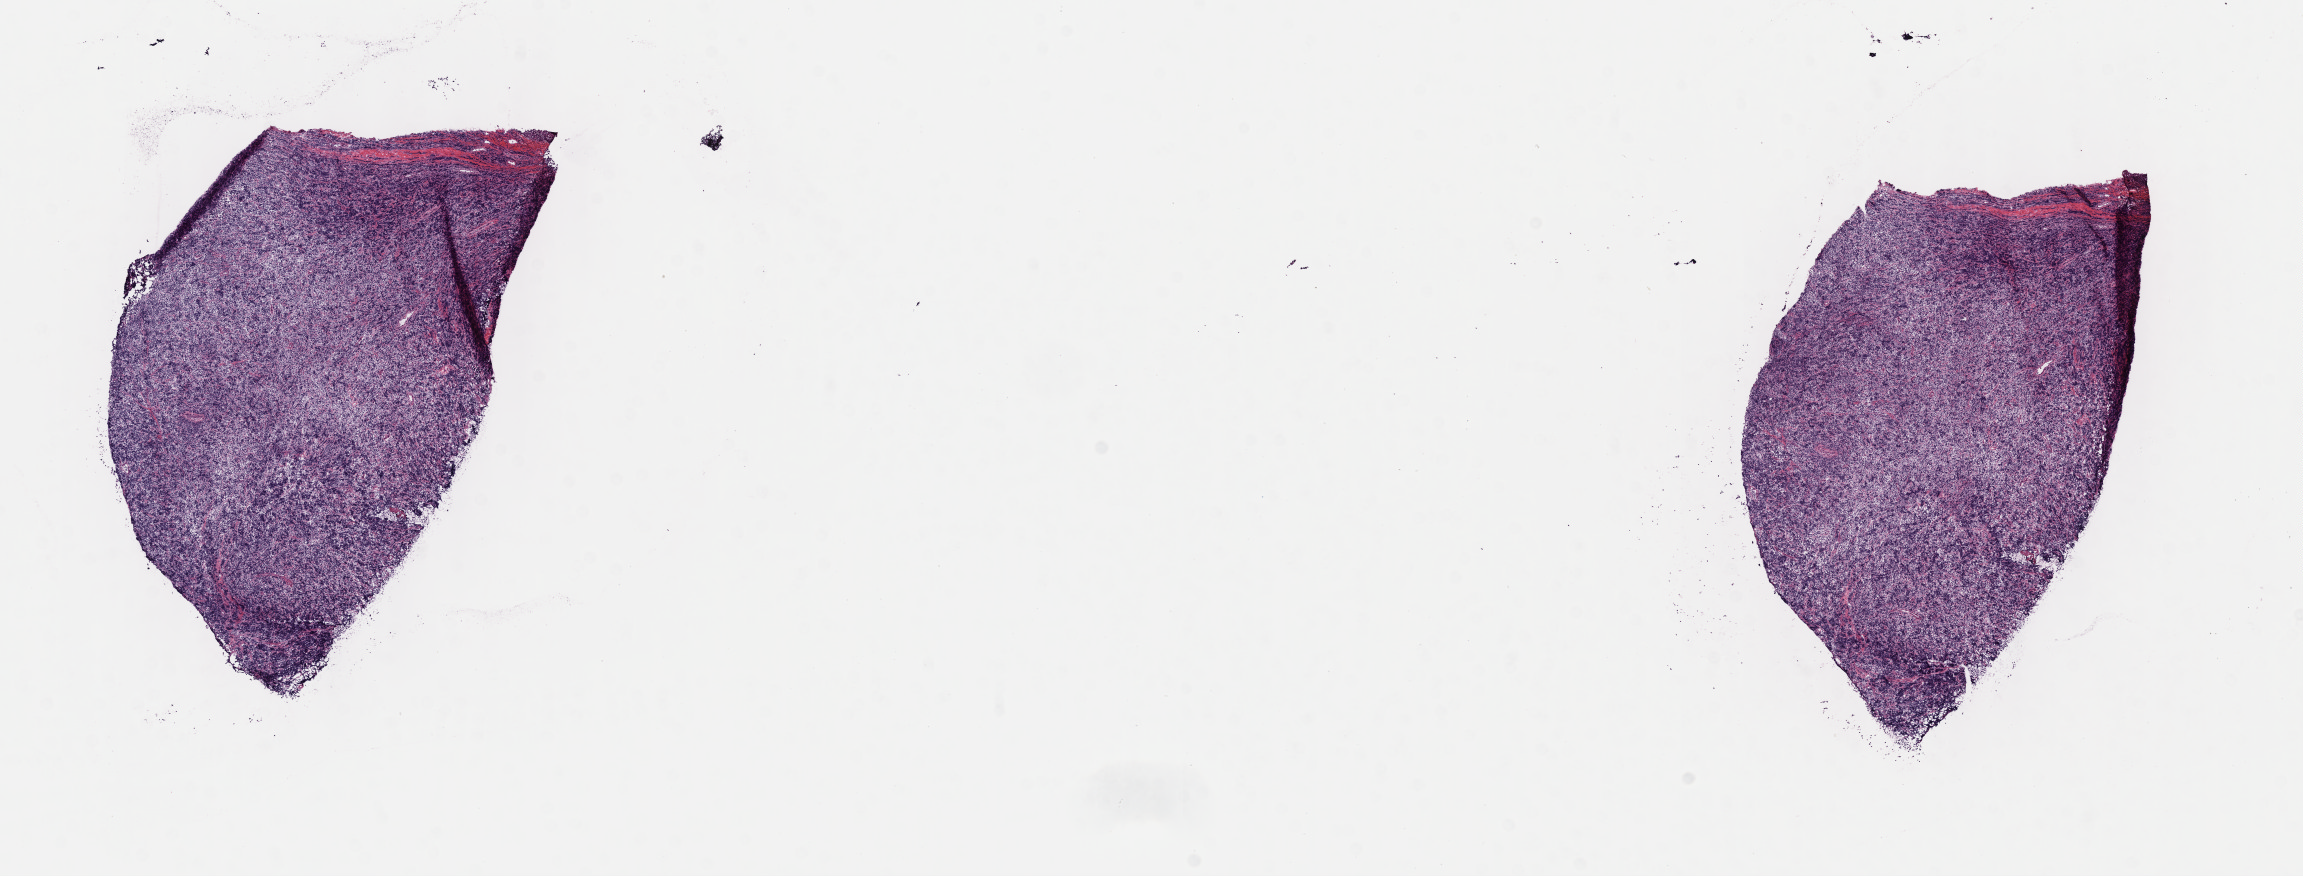
Hematoxylin and eosin (H&E) whole-slide image — a low-resolution overview of the entire scanned area, about 18.6 x 7.1 mm; frozen section; specimen: primary tumor; anatomic site: cranium. Patient: male, age at initial diagnosis 6 years. Composition of this section per pathologist review: tumor cells 90%, tumor nuclei 90%, stromal cells 7%, necrosis 3%, normal cells 0%. Inflammatory infiltration, as recorded: lymphocyte infiltration 2%, monocyte infiltration 5%, neutrophil infiltration 0%.
• Ann Arbor stage (patient): Stage III
• diagnosis: Burkitt lymphoma, NOS